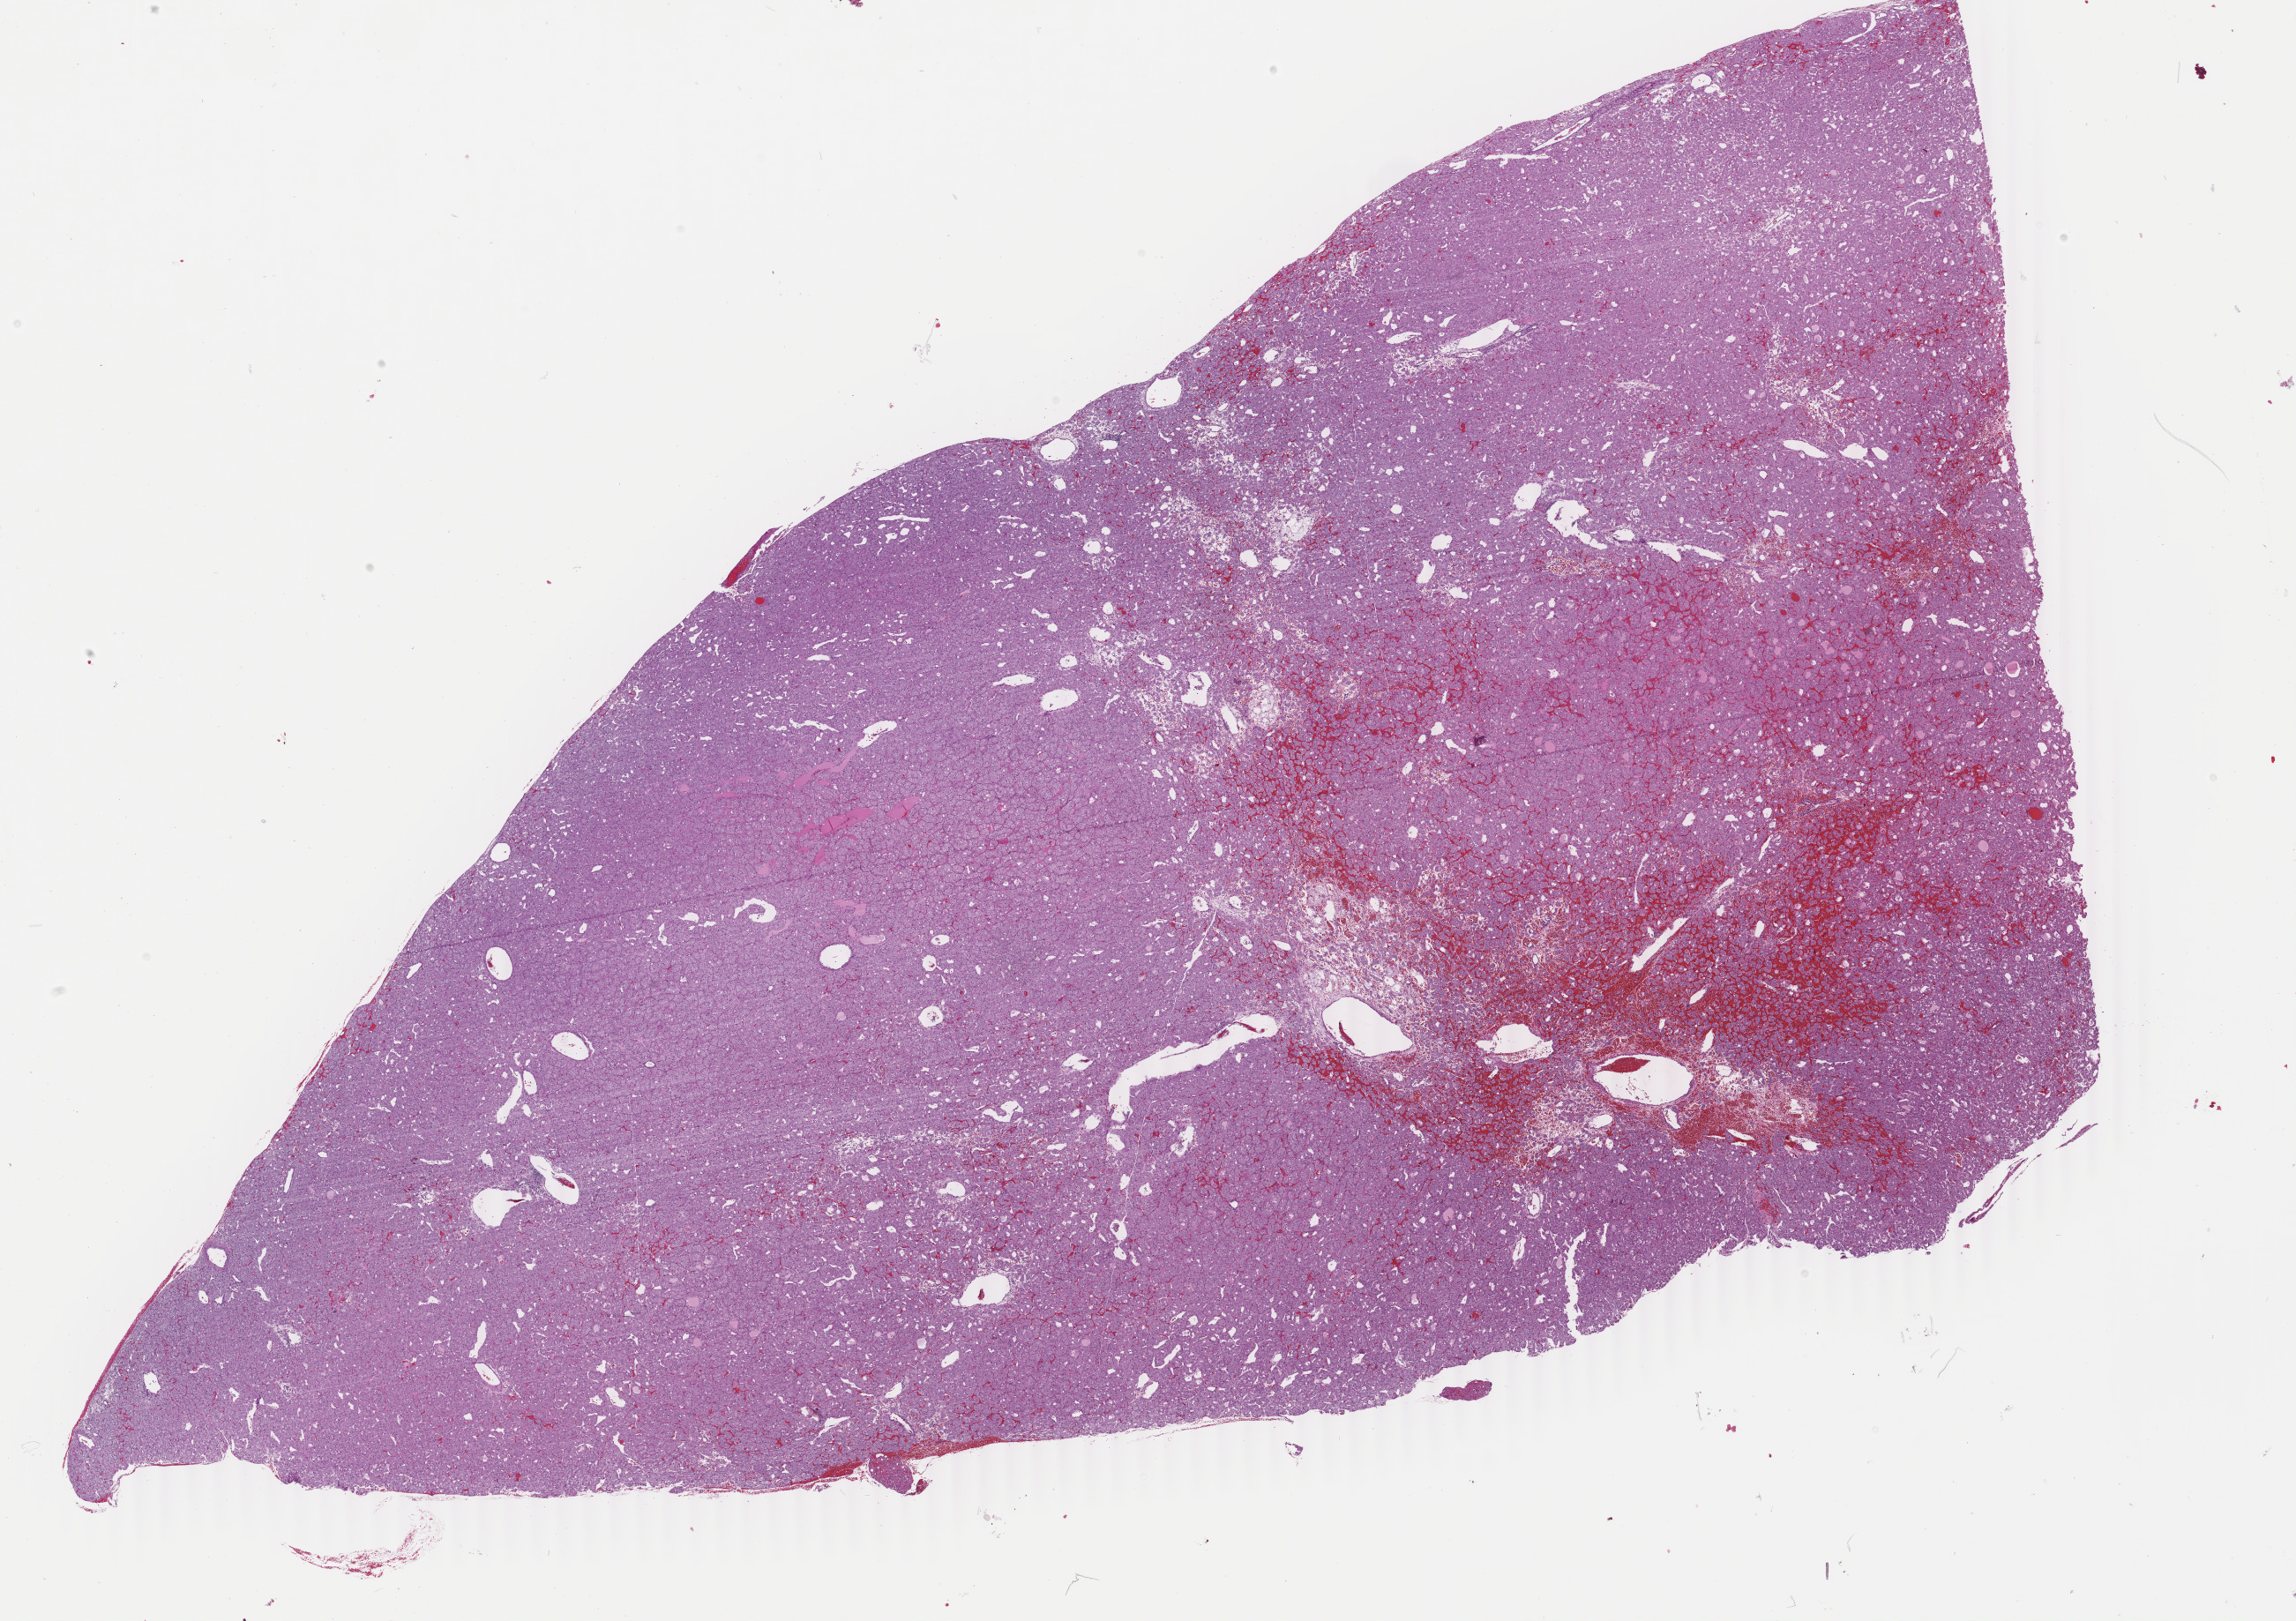
Digitized Hematoxylin and eosin (H&E) stained tissue section (whole slide) — a low-resolution overview of the entire scanned area, about 20.7 x 14.6 mm (acquisition: 40x scan), formalin-fixed paraffin-embedded (FFPE) diagnostic section, primary tumour sample from the kidney. Patient: male, age at initial diagnosis 30 years.
Diagnosis: Renal cell carcinoma, chromophobe type.